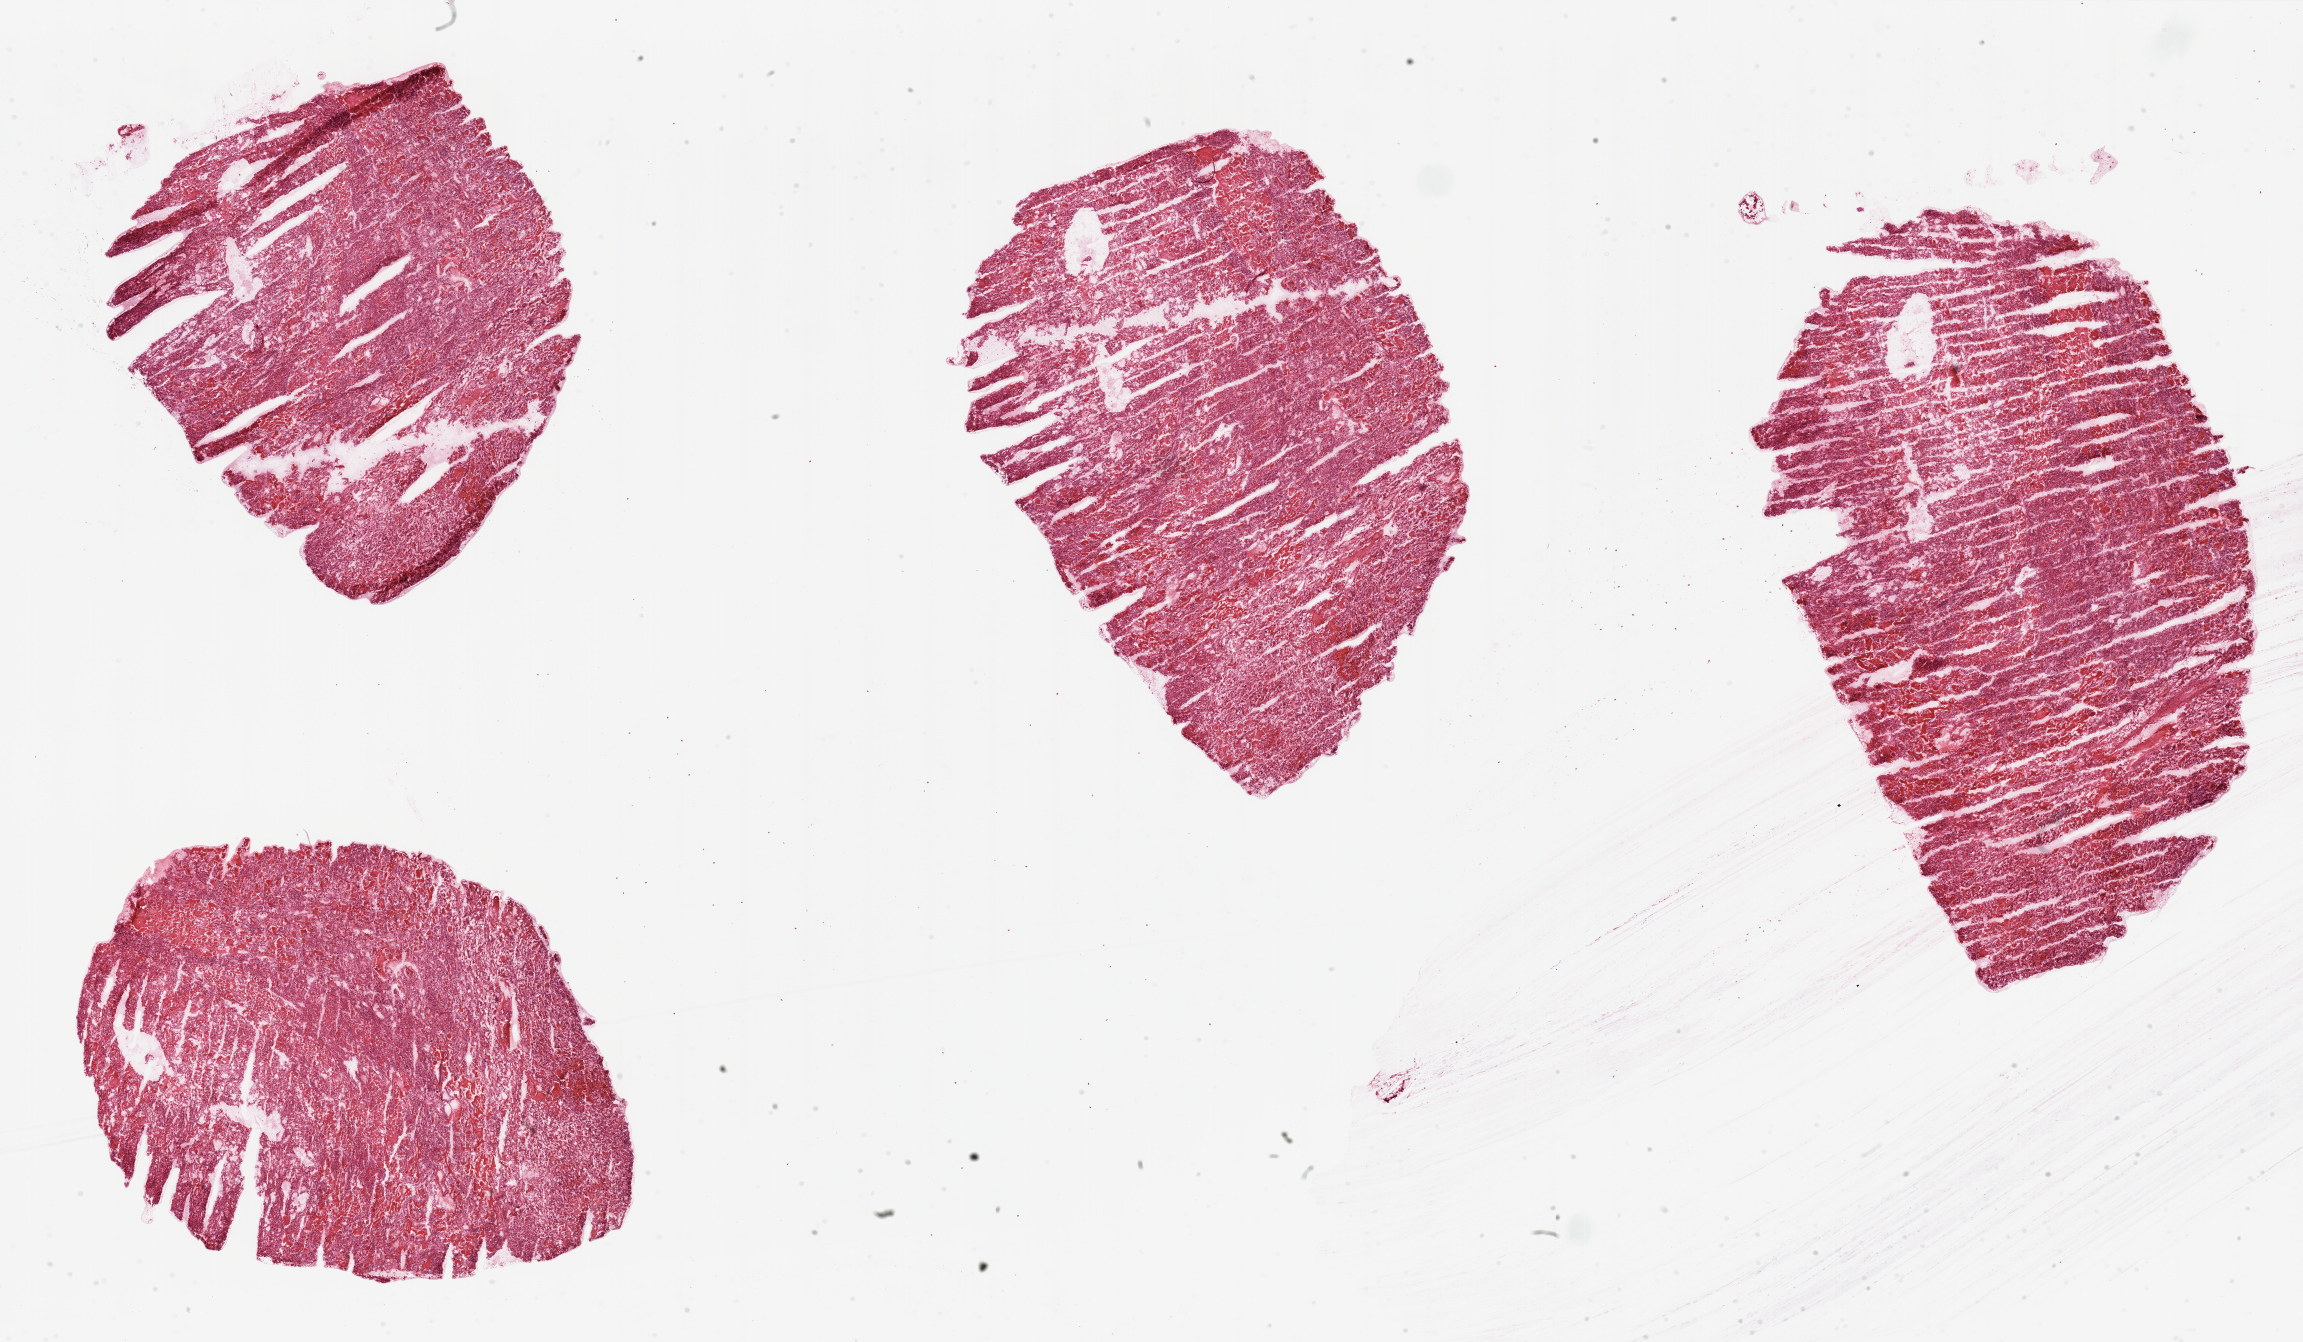
H&E whole-slide image, whole scanned area (about 36.4 x 21.2 mm) shown as a low-resolution overview. Tumour tissue sample, sampled site: kidney. Patient: female, age 69 years. Histologic grade: G3 (poorly differentiated). Composition of this section per pathologist review: tumour nuclei 90%, necrosis 10%.
AJCC pathologic stage: III. Primary tumour site (as recorded): upper pole. Diagnosis: Renal cell carcinoma, NOS.